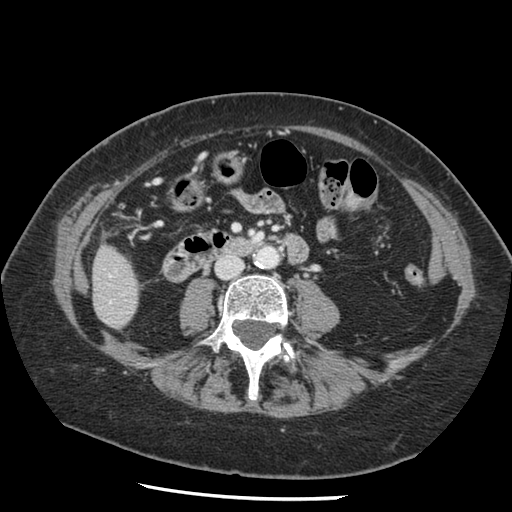
Contrast-enhanced abdominal CT, one axial slice. Slice 24 of 148 in the series (ordered by position). Intravenous contrast given. Soft-tissue window (W 400 / L 40 HU). 2.5 mm slice thickness. 512 × 512 image matrix, field of view 330 × 330 mm. Female patient, age 85 years. Case-level facts recorded for this patient, not image findings: diagnosis: colorectal cancer liver metastases, imaged before liver resection; multiple liver metastases: no; largest metastasis: 0.9 cm; disease in both lobes: no.
Structures marked on this image (outlined manually by an expert reader):
- liver: bounding box (x1, y1, x2, y2) in pixels: (93, 247, 139, 328)
- planned liver remnant (the part of the liver to remain after resection): (93, 247, 139, 328)